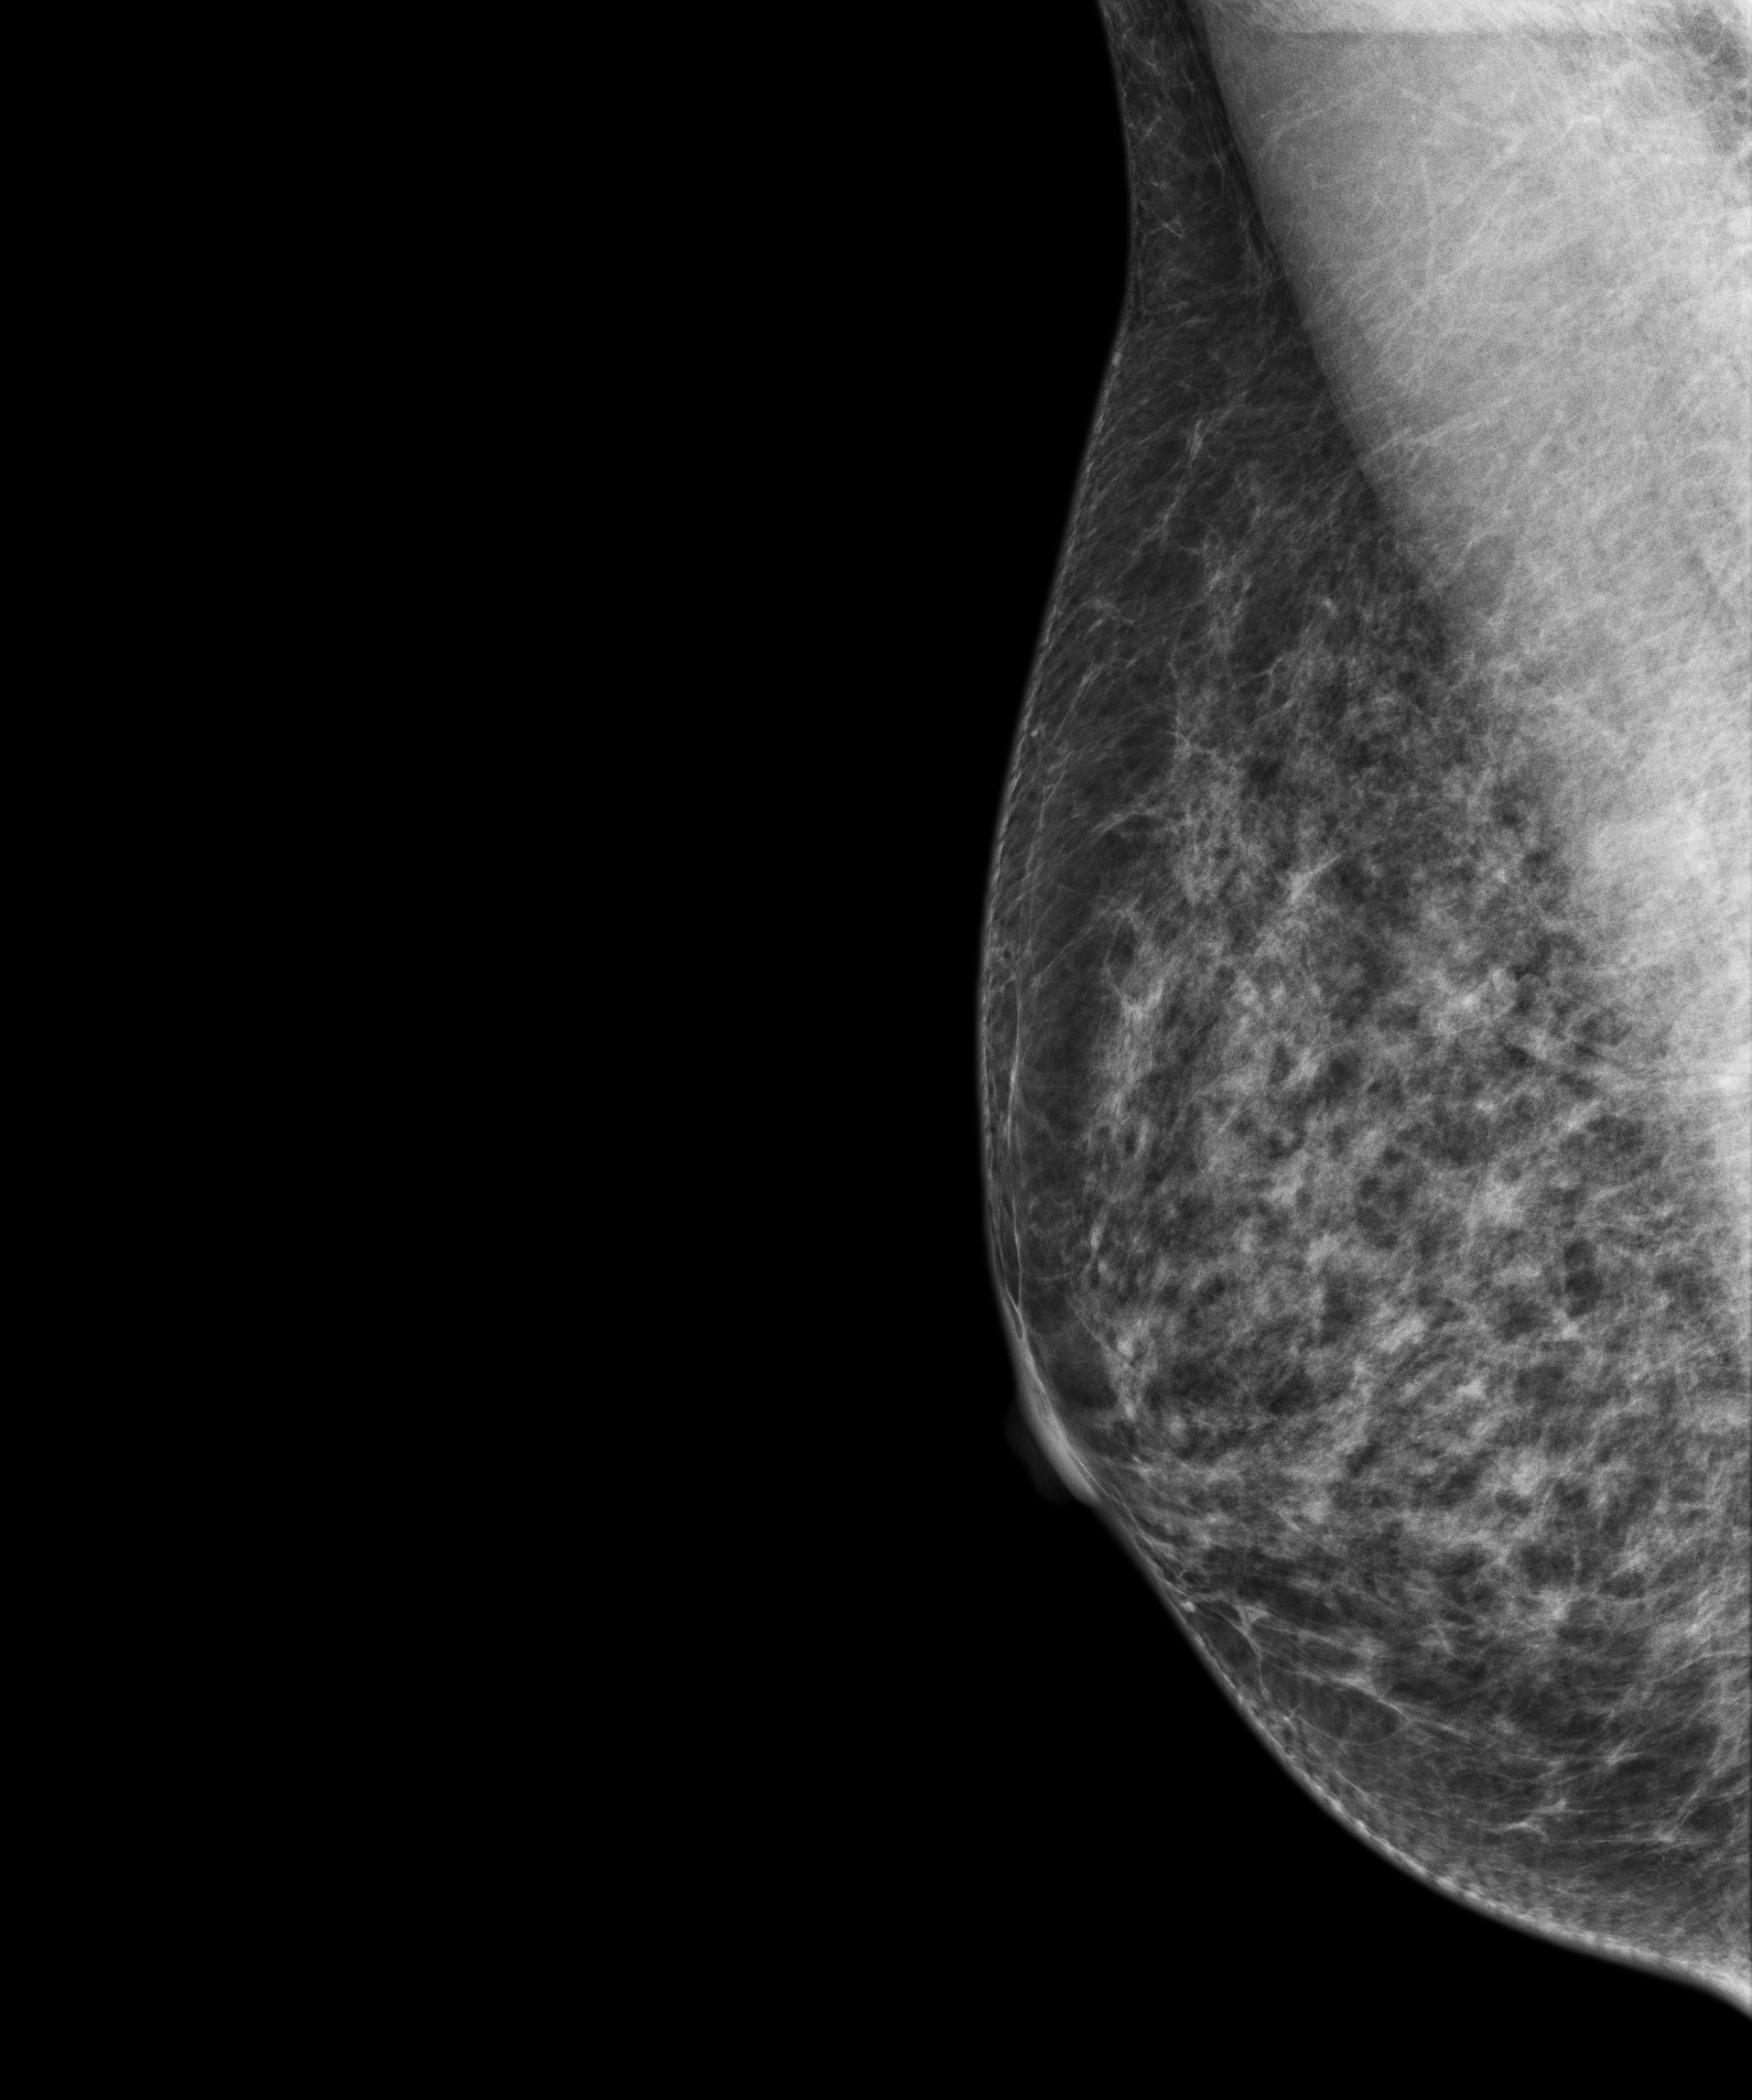
Annual screening mammography examination; system: Senographe Essential ADS_56.21.3. Patient: female, 70 years.
Image type: full-field digital mammogram. Breast: right. Projection: mediolateral oblique (MLO) view.